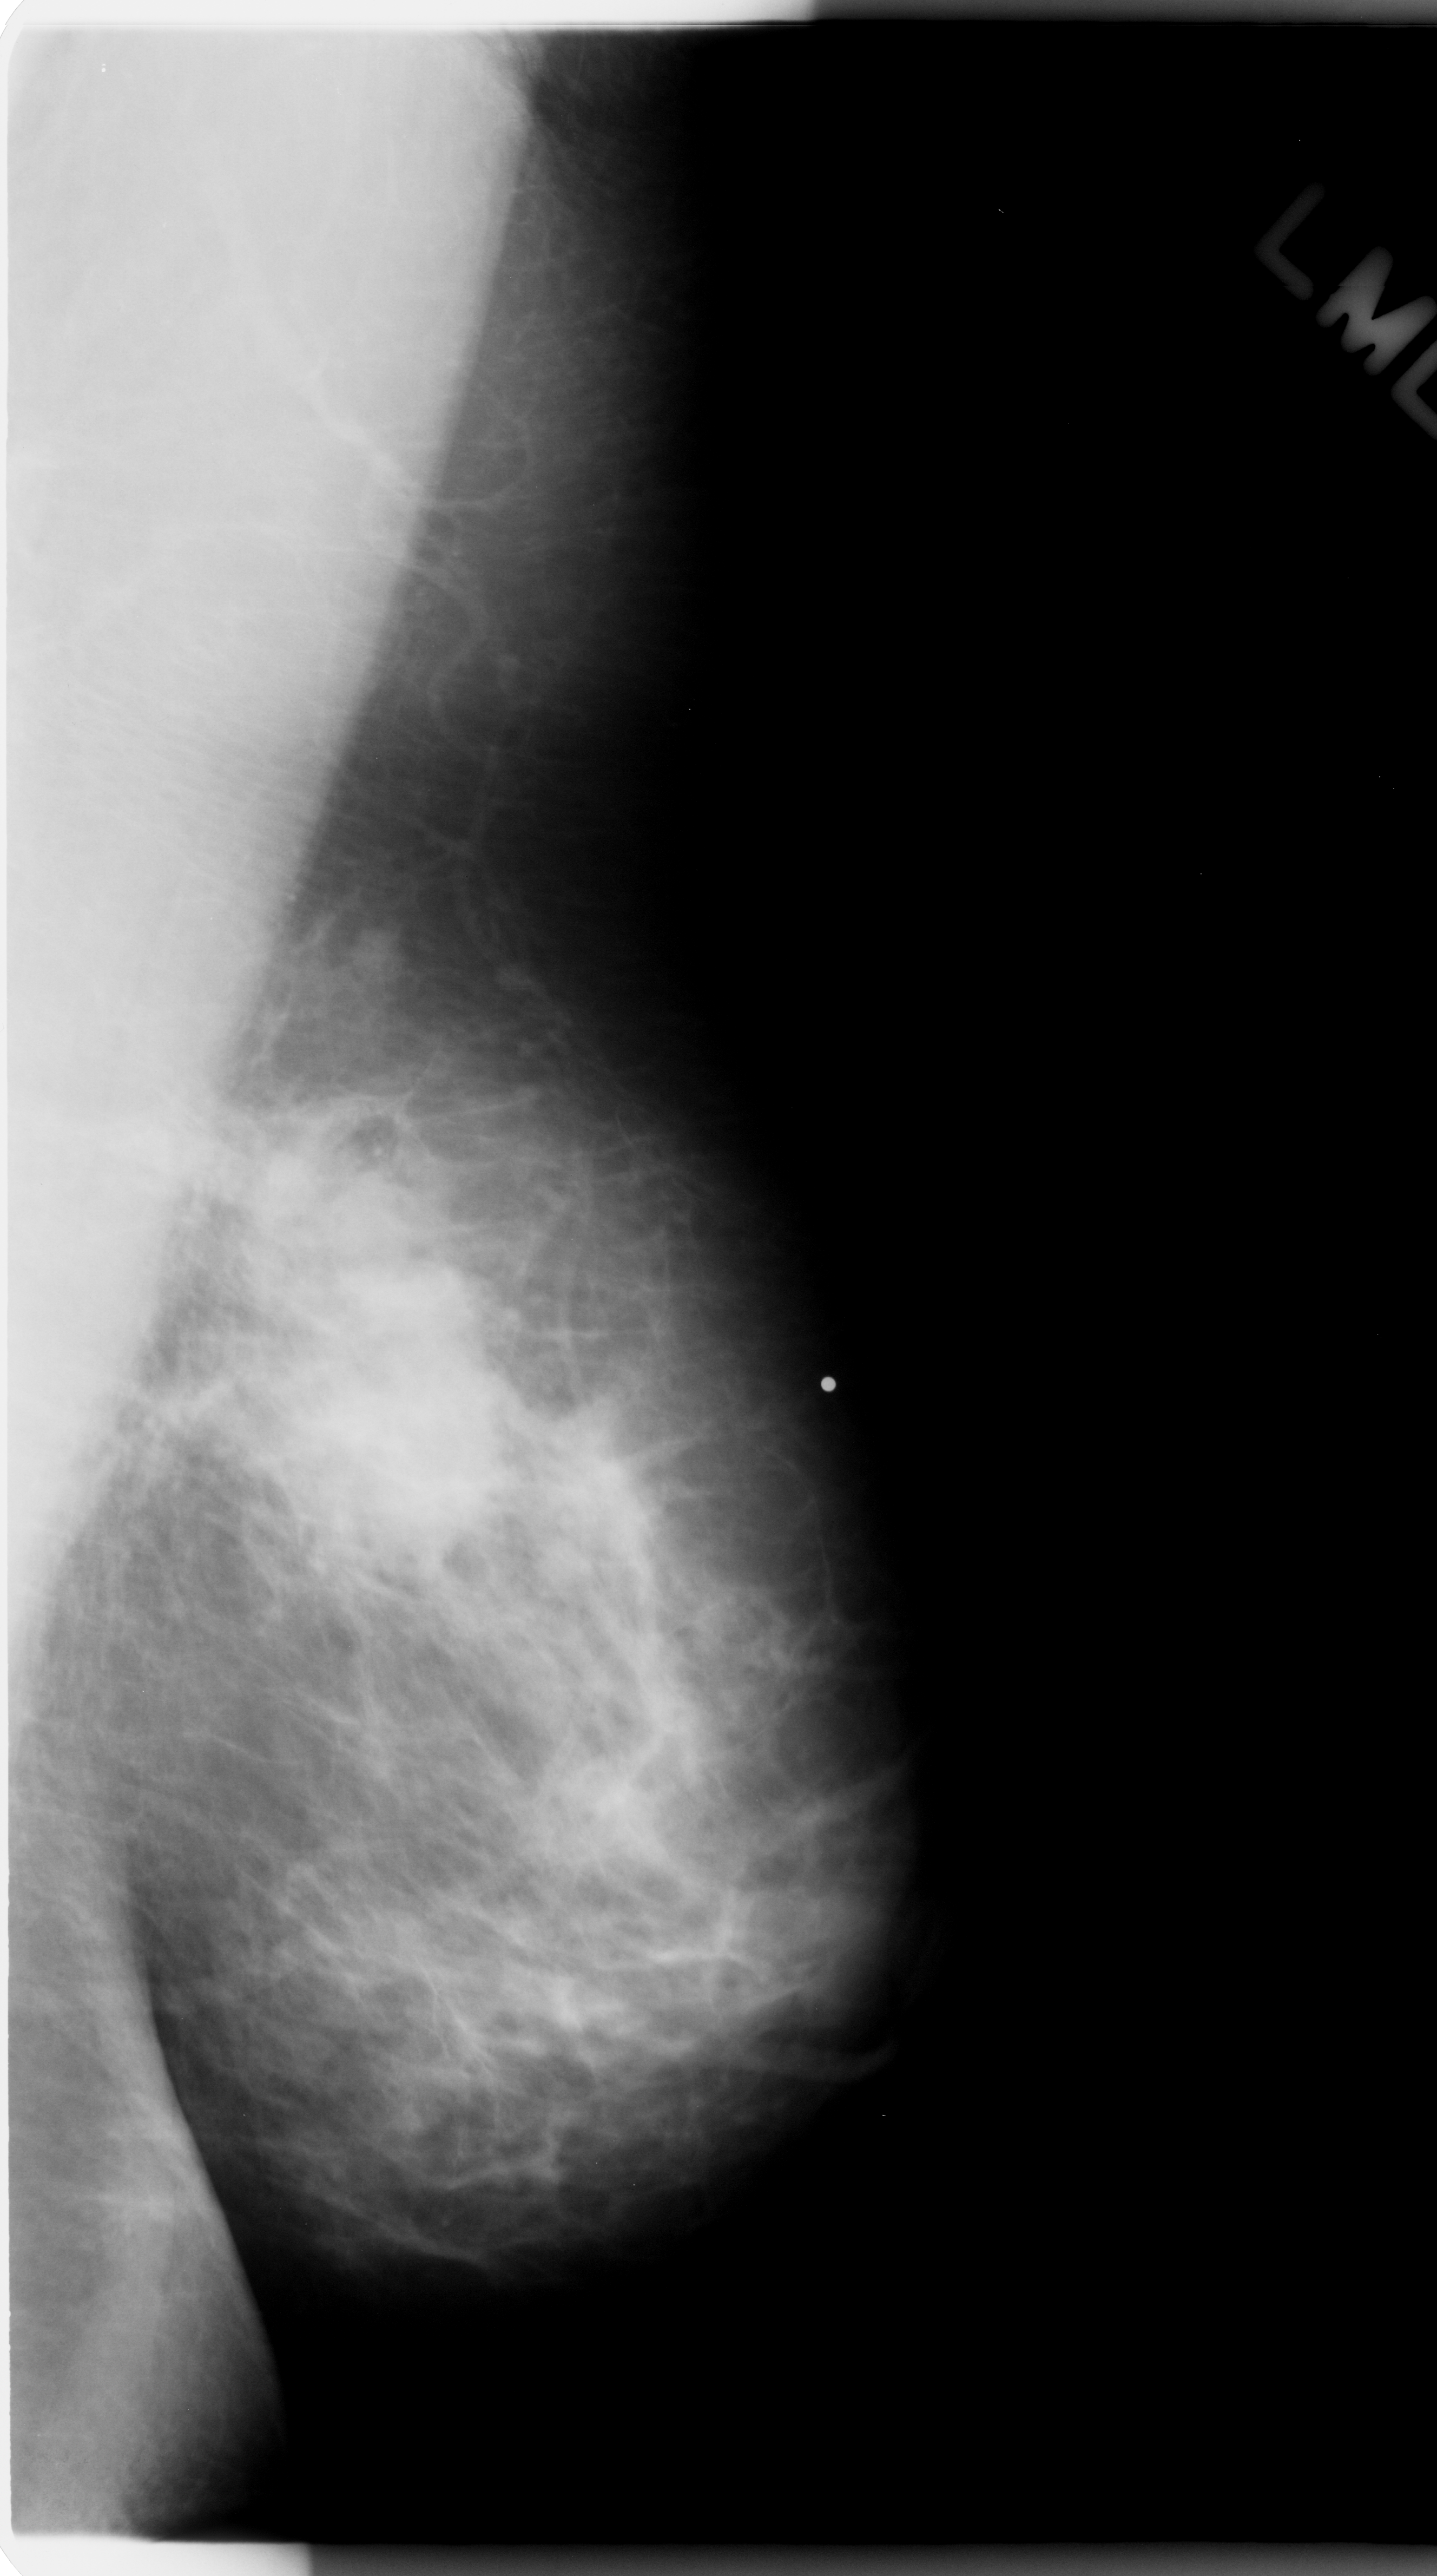
Mammogram (digitized film), left breast, mediolateral oblique (MLO) view, BI-RADS breast density category 2 (scale 1–4).
Marked abnormality: mass, shape irregular, margins ill defined; BI-RADS assessment category 5; pathology result (as recorded, not read from the image): malignant.